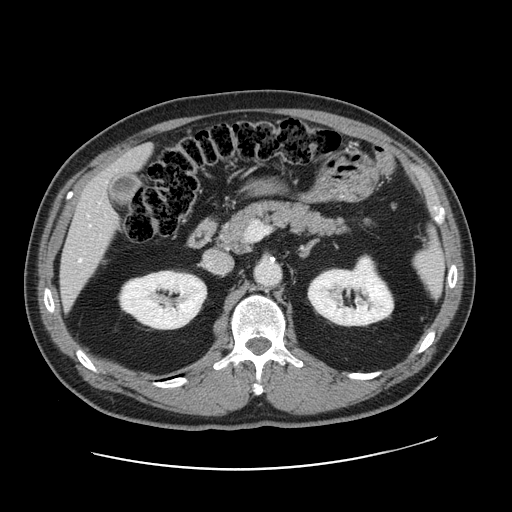
Contrast-enhanced abdominal CT, one axial slice; position 83 of 178 along the scan axis; 120 kVp; soft-tissue window (W 400 / L 40 HU); 2.5 mm slice thickness; 512 × 512 image matrix. Male patient, age 63 years. Case-level facts recorded for this patient, not image findings: diagnosis: colorectal cancer liver metastases, imaged before liver resection.
Annotated regions visible in this slice (outlined manually by an expert reader):
- hepatic veins: box from (x=79, y=258) to (x=82, y=261) px
- liver: (x=61, y=147)–(x=151, y=303)
- planned liver remnant (the part of the liver to remain after resection): (x=111, y=146)–(x=151, y=173)